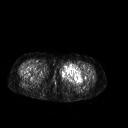
FDG PET of an extremity soft-tissue mass (from a PET/CT study), one axial slice. Position 244 of 267 along the scan axis. 3.27 mm slice thickness. 128 × 128 image matrix. Patient: female, 42 years. Case-level facts recorded for this patient, not image findings: histological type: pleiomorphic leiomyosarcoma; grade: intermediate; site of the primary tumour: left thigh.
Outlined on this slice (expert contour drawn on MRI and transferred to this co-registered scan by the dataset authors):
- gross tumour volume including surrounding oedema: bounding box (x1, y1, x2, y2) in pixels: (59, 64, 82, 82)
- gross tumour volume (mass): (59, 64, 82, 82)